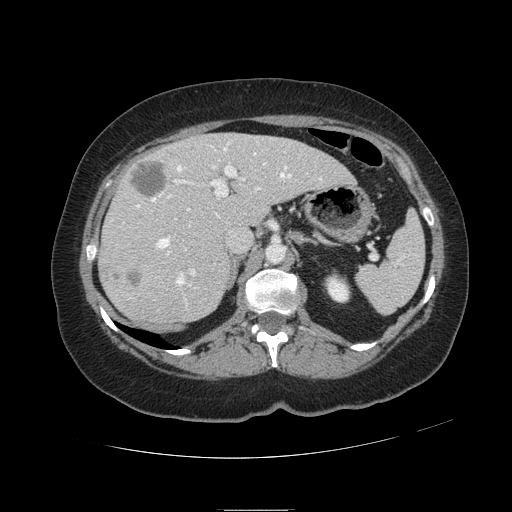
Contrast-enhanced abdominal CT, one axial slice; 120 kVp; intravenous contrast given; soft-tissue window (W 400 / L 40 HU); 2.5 mm slice thickness; 512 × 512 image matrix, field of view 400 × 400 mm. Female patient, age 52 years. Case-level facts recorded for this patient, not image findings: diagnosis: colorectal cancer liver metastases, imaged before liver resection; multiple liver metastases: yes; largest metastasis: 6.3 cm; chemotherapy before resection: yes.
Annotated regions visible in this slice (manually delineated by an expert):
- hepatic veins: bounding box [x1, y1, x2, y2] px = [137, 143, 322, 304]
- liver: [100, 134, 352, 323]
- planned liver remnant (the part of the liver to remain after resection): [167, 134, 353, 225]
- portal vein (with intrahepatic branches): [123, 163, 266, 275]
- liver metastasis: [130, 160, 167, 197]
- liver metastasis: [127, 268, 142, 288]